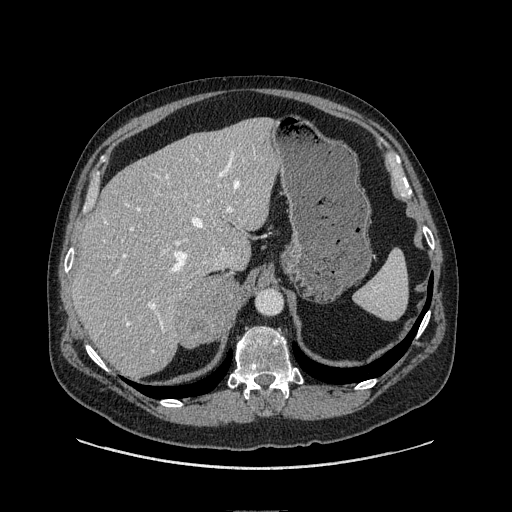
Contrast-enhanced abdominal CT, one axial slice; slice 77 of 149 in the series (ordered by position); soft-tissue window (W 400 / L 40 HU); 1.25 mm slice thickness; 512 × 512 image matrix, field of view 440 × 440 mm. Male patient. Case-level facts recorded for this patient, not image findings: diagnosis: adrenocortical carcinoma; tumour side: right adrenal; tumour size at pathology: 7.5 cm; Ki-67 index: 15 %; stage (as recorded): 2.
Annotated regions visible in this slice (semi-automatically segmented with operator editing):
- mass: box from (x=179, y=275) to (x=242, y=346) px